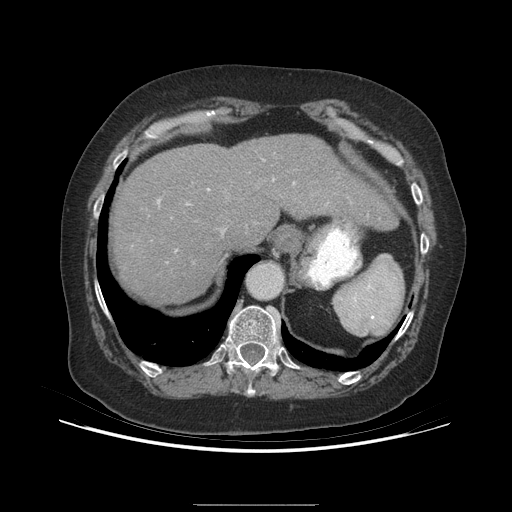
Contrast-enhanced abdominal CT (liver protocol), one axial slice; slice 172 of 192 in the series (ordered by position); soft-tissue window (W 400 / L 40 HU); 2.5 mm slice thickness; 512 × 512 image matrix, field of view 400 × 400 mm. Case-level facts recorded for this patient, not image findings: diagnosis: hepatocellular carcinoma (patient treated with transarterial chemoembolisation; whether this scan precedes or follows treatment is not stated here); TNM stage (as recorded): Stage-I; Child-Pugh class: A; tumour differentiation: moderately differentiated; tumour nodularity: uninodular.
Outlined on this slice (semi-automatically segmented with operator editing):
- liver parenchyma outside the tumour (the mass and vessels are separate outlines, so this box may not span the whole liver): bounding box <112,134,396,302> (left, top, right, bottom; pixels)
- liver vessels: <158,200,160,203>